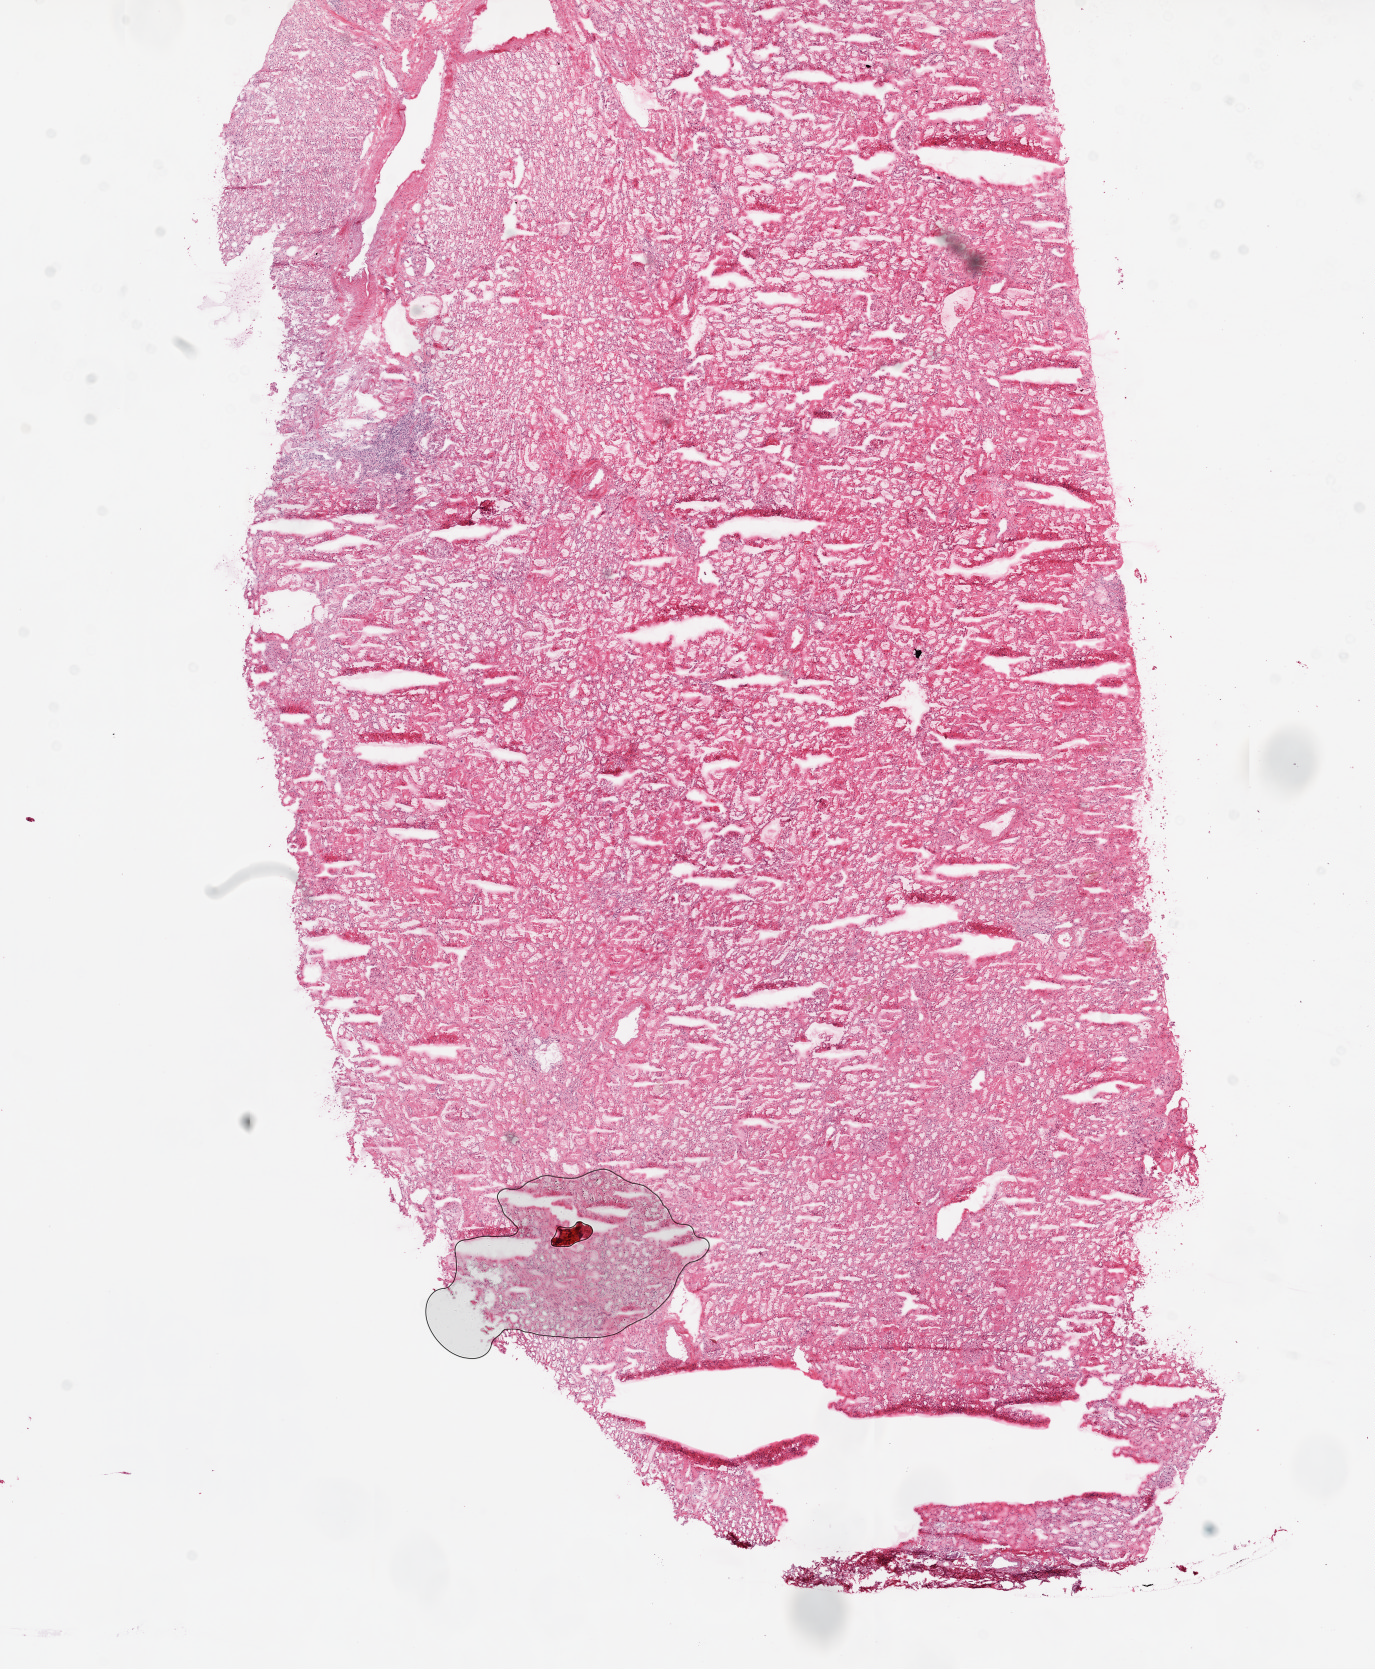
Whole-slide histology image, H&E — low-resolution overview of the scanned area, about 11.0 x 13.4 mm (from a 20x scan); frozen section; kidney, solid tissue normal (non-tumour tissue) sample. Male, age 69 years at initial diagnosis.
This section: solid tissue normal sample (biorepository sample class). Patient diagnosis: Clear cell adenocarcinoma, NOS.